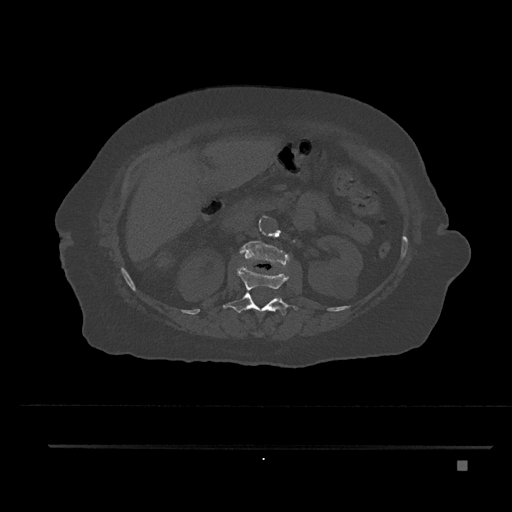
CT including the spine, one axial slice. Slice 214 of 797 in the series (ordered by position). 120 kVp. Bone window (W 1800 / L 400 HU). 512 × 512 image matrix, field of view 437 × 437 mm. Patient: female, 76 years. Case-level facts recorded for this patient, not image findings: primary cancer: lung; vertebrae with lytic lesions (as recorded): T11, L3.
Annotated regions visible in this slice (semi-automatic segmentation, software-assisted and operator-edited):
- L1 vertebra: bounding box [x1, y1, x2, y2] px = [223, 265, 298, 317]
- L2 vertebra: [240, 240, 290, 265]